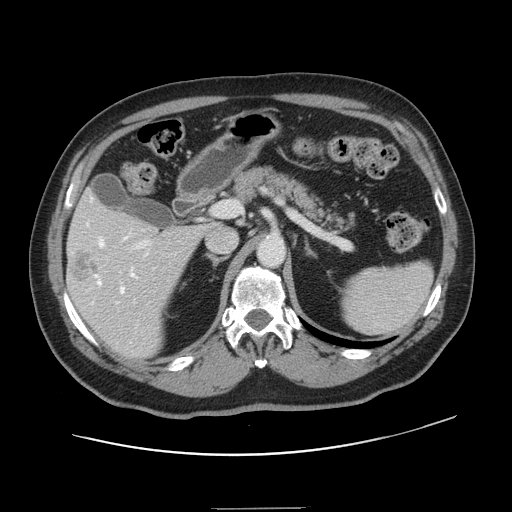
Contrast-enhanced abdominal CT, one axial slice. Position 82 of 143 along the scan axis. Intravenous contrast given. Soft-tissue window (W 400 / L 40 HU). 512 × 512 image matrix. Male patient, age 62 years. Case-level facts recorded for this patient, not image findings: diagnosis: colorectal cancer liver metastases, imaged before liver resection; multiple liver metastases: yes; largest metastasis: 2.7 cm; chemotherapy before resection: yes.
Outlined on this slice (outlined manually by an expert reader):
- hepatic veins: bounding box (x1, y1, x2, y2) in pixels: (91, 198, 146, 294)
- liver: (67, 194, 207, 359)
- planned liver remnant (the part of the liver to remain after resection): (70, 194, 141, 236)
- portal vein (with intrahepatic branches): (116, 205, 220, 303)
- liver metastasis: (72, 253, 100, 282)